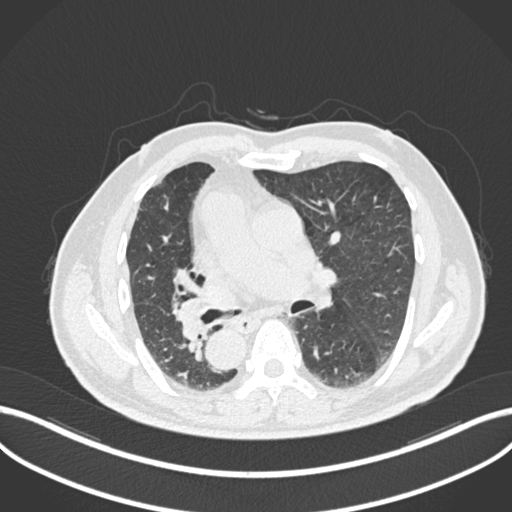
Chest CT, one axial slice. Slice 121 of 206 in the series (ordered by position). 120 kVp. Lung window (W 1500 / L -600 HU). 1 mm slice thickness. 512 × 512 image matrix, field of view 400 × 400 mm. Patient: male, 67 years. From the clinical record (not read from this slice): clinical TNM (as recorded): T2a N0 M0.
Structures marked on this image (bounding box drawn by a radiologist):
- lung tumour (recorded histology: squamous cell carcinoma): bounding box (x1, y1, x2, y2) in pixels: (171, 293, 210, 342)